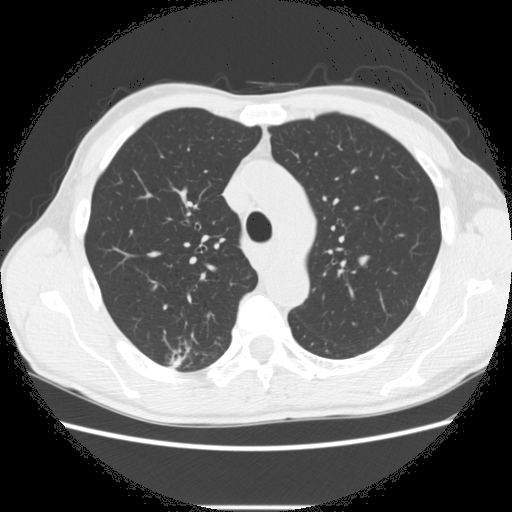
Chest CT (low-dose screening protocol), one axial image, second screening round (one year after baseline), lung window (W 1500 / L -600 HU), 120 kVp, 512 × 512 image matrix, field of view 360 × 360 mm. Male, age 66 years at enrolment. Former smoker at enrolment.
Expert-annotated lung lesion, bounding box [x1, y1, x2, y2] px = [162, 339, 221, 377]. The screening reader recorded 5 non-calcified nodules or masses ≥4 mm on this exam (right lower lobe, right upper lobe, right upper lobe, right upper lobe, left lower lobe); which of them this box marks is not recorded. Lung cancer was diagnosed 75 days after this screen: adenocarcinoma, NOS, right upper lobe, undifferentiated (G4), stage IA (AJCC 6th edition), 20 mm at pathology.